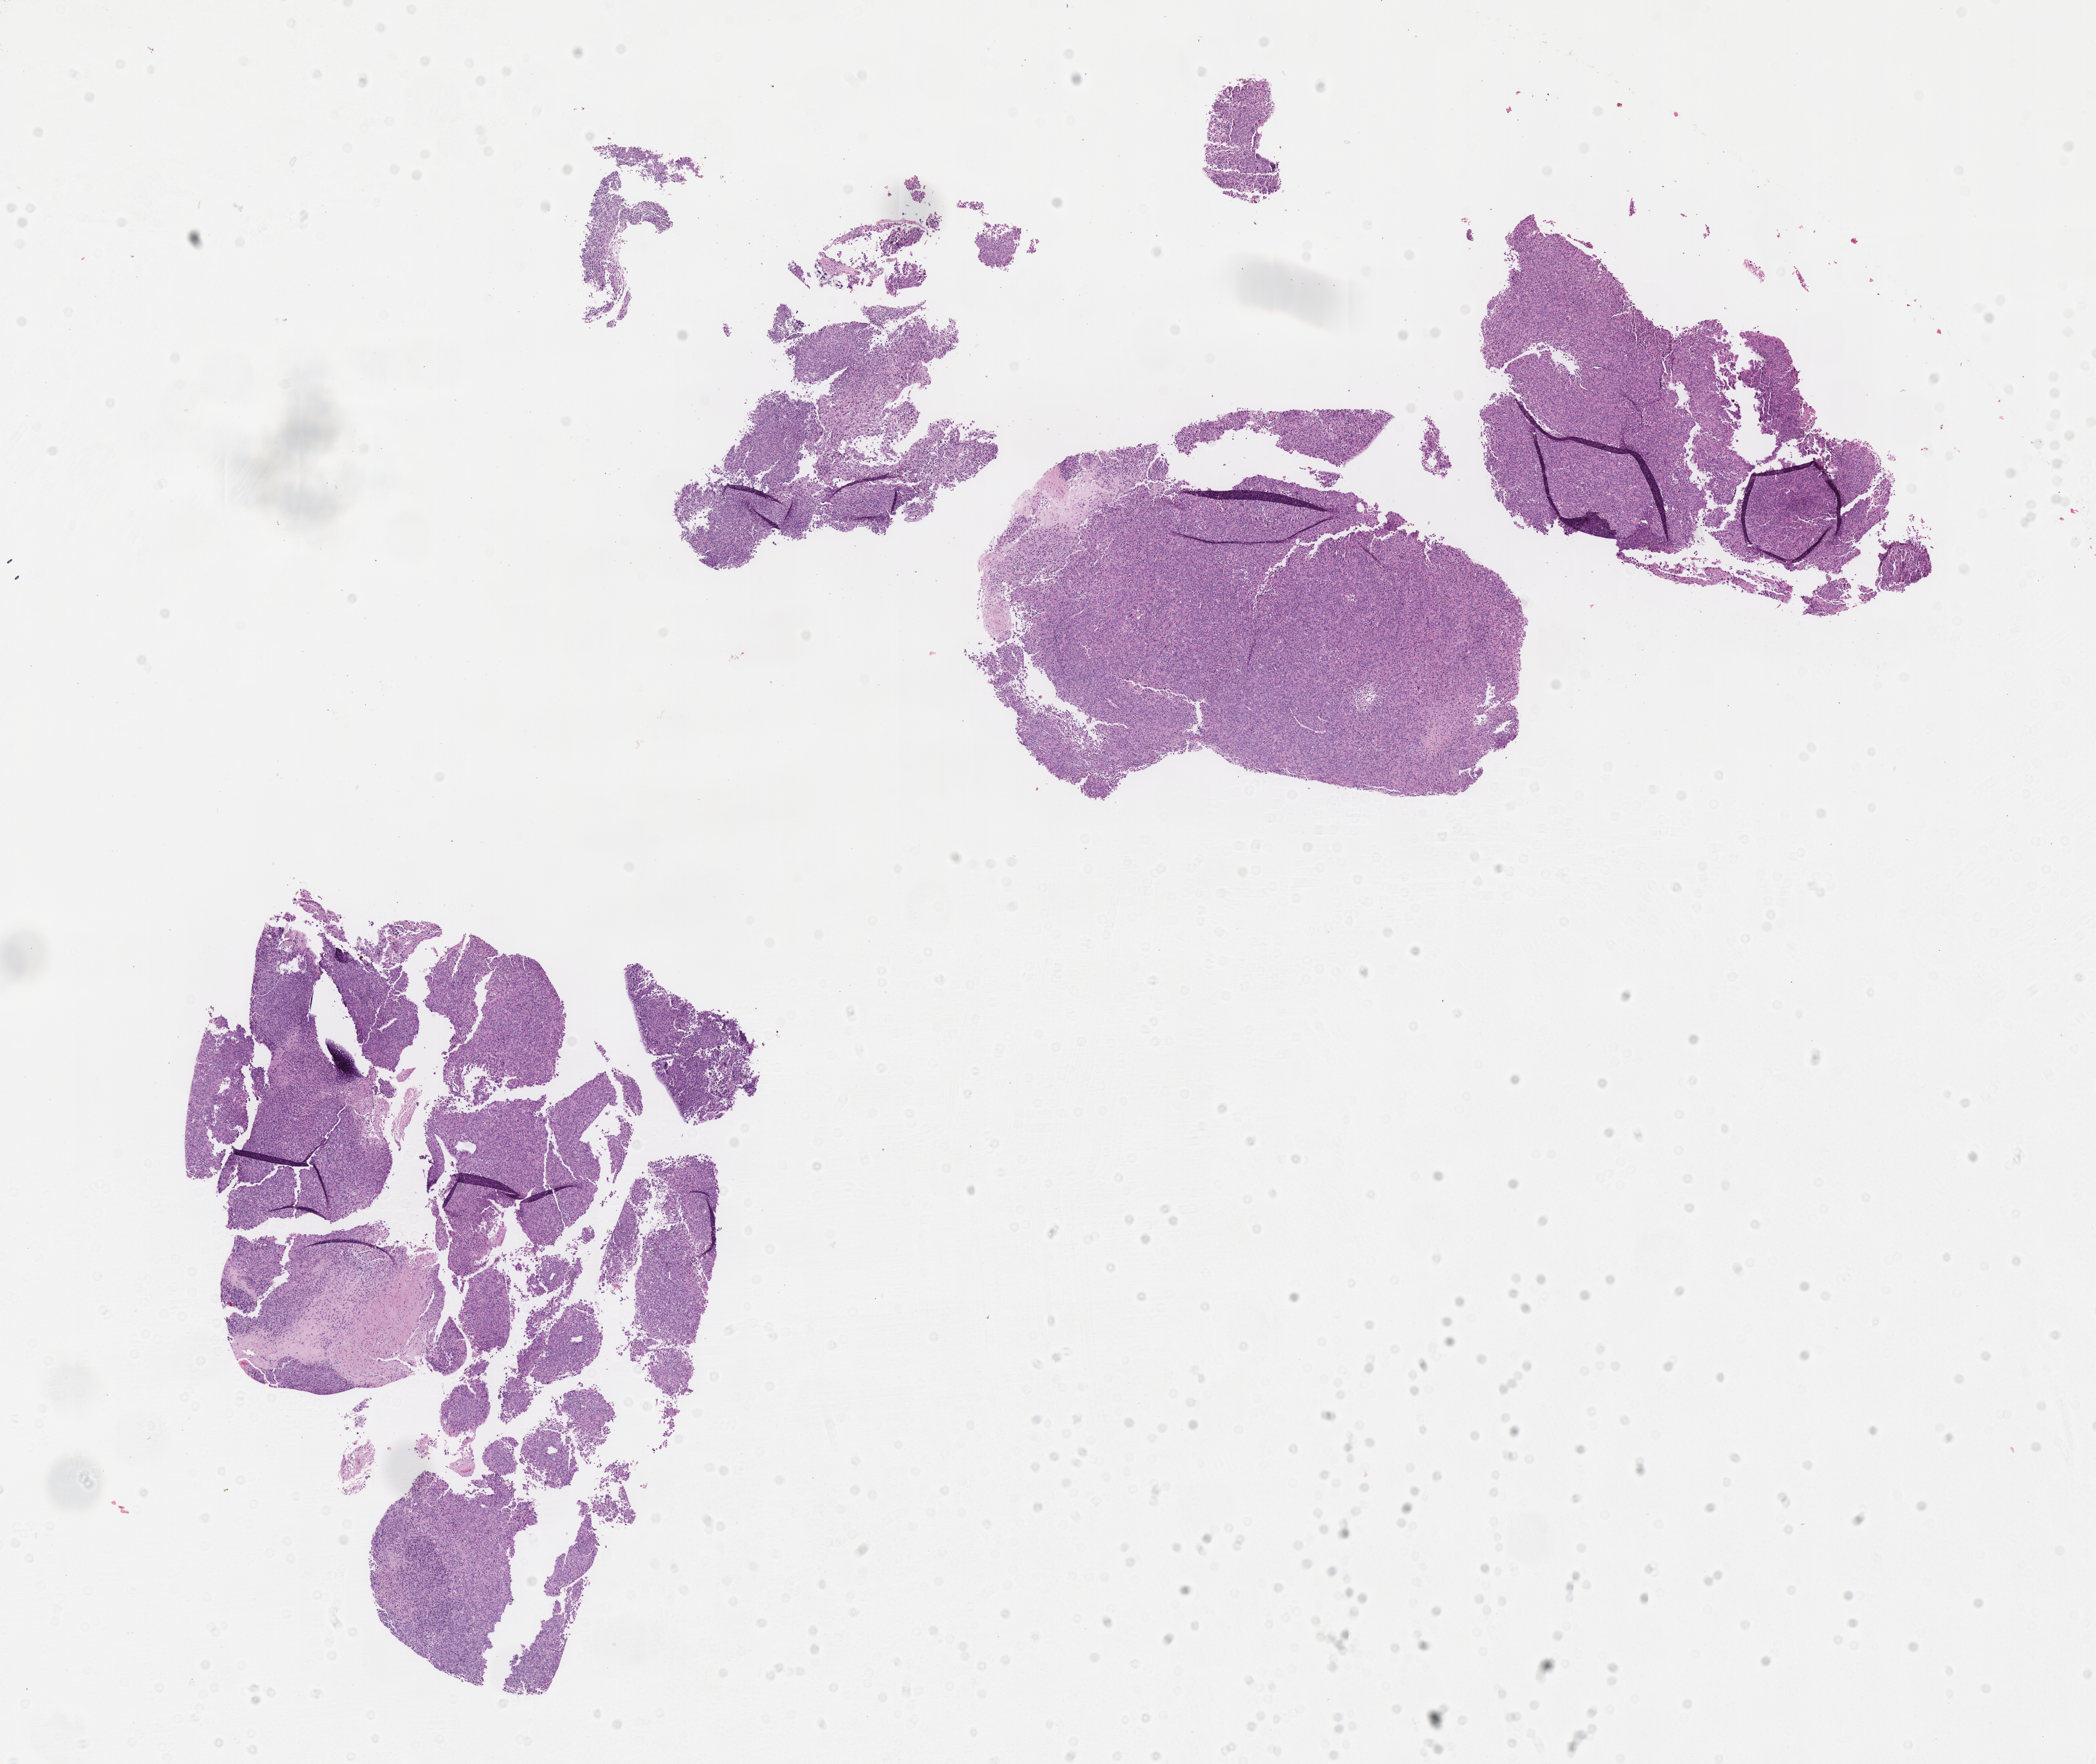
Hematoxylin and eosin (H&E) whole-slide image of tumor tissue — a low-resolution overview of the entire scanned area, about 14.1 x 11.9 mm; formalin-fixed paraffin-embedded section; site: soft tissue, forearm-left. Female patient, age at diagnosis 19.8 years.
Stage (as recorded): 3. Metastatic status at presentation (as recorded): non-metastatic. Diagnosis: rhabdomyosarcoma; histological classification: embryonal rhabdomyosarcoma.